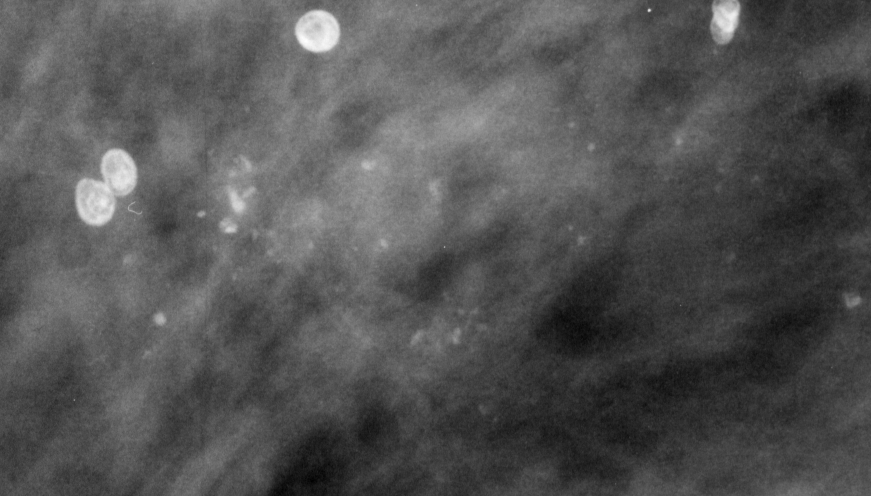
Crop from a digitized film mammogram around one marked abnormality, left breast, MLO view.
Calcifications, morphology pleomorphic, distribution segmental; BI-RADS assessment category 4; subtlety rating 3 on a 1 (subtle) to 5 (obvious) scale; pathology (as recorded): malignant.